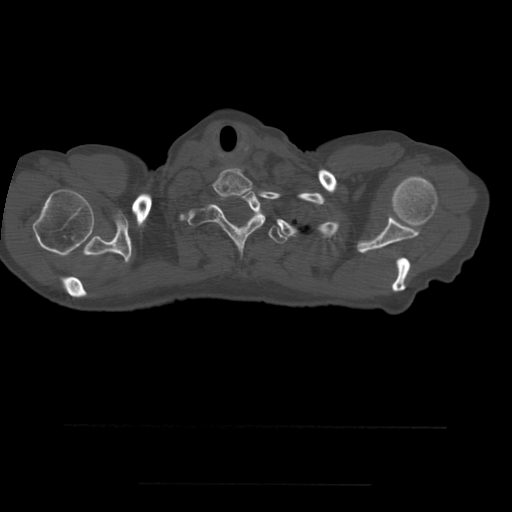
CT including the spine, one axial slice; slice 446 of 544 in the series (ordered by position); bone window (W 1800 / L 400 HU); 1.25 mm slice thickness; 512 × 512 image matrix, field of view 350 × 350 mm. Patient age 58 years. From the clinical record (not read from this slice): primary cancer: lung.
Structures marked on this image (semi-automatic segmentation, software-assisted and operator-edited):
- T1 vertebra: bounding box [x1, y1, x2, y2] px = [187, 191, 266, 253]
- T2 vertebra: [261, 213, 289, 244]